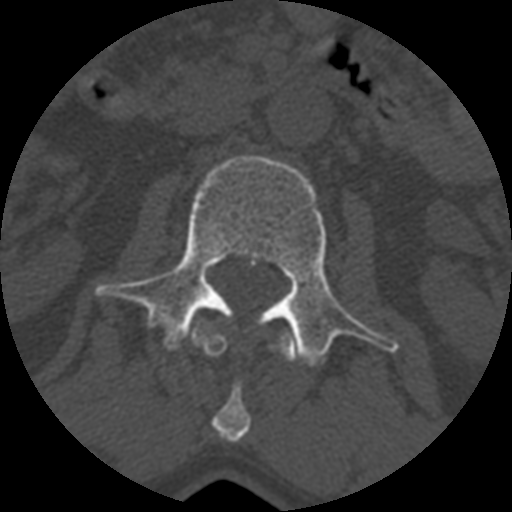
CT including the spine, one axial slice; position 338 of 399 along the scan axis; reconstruction kernel STANDARD; bone window (W 1800 / L 400 HU); 1.25 mm slice thickness; 512 × 512 image matrix, field of view 160 × 160 mm. Patient age 71 years. From the clinical record (not read from this slice): primary cancer: prostate.
Structures marked on this image (semi-automatically segmented with operator editing):
- L1 vertebra: bounding box <192,322,296,440> (left, top, right, bottom; pixels)
- L2 vertebra: <96,155,399,366>